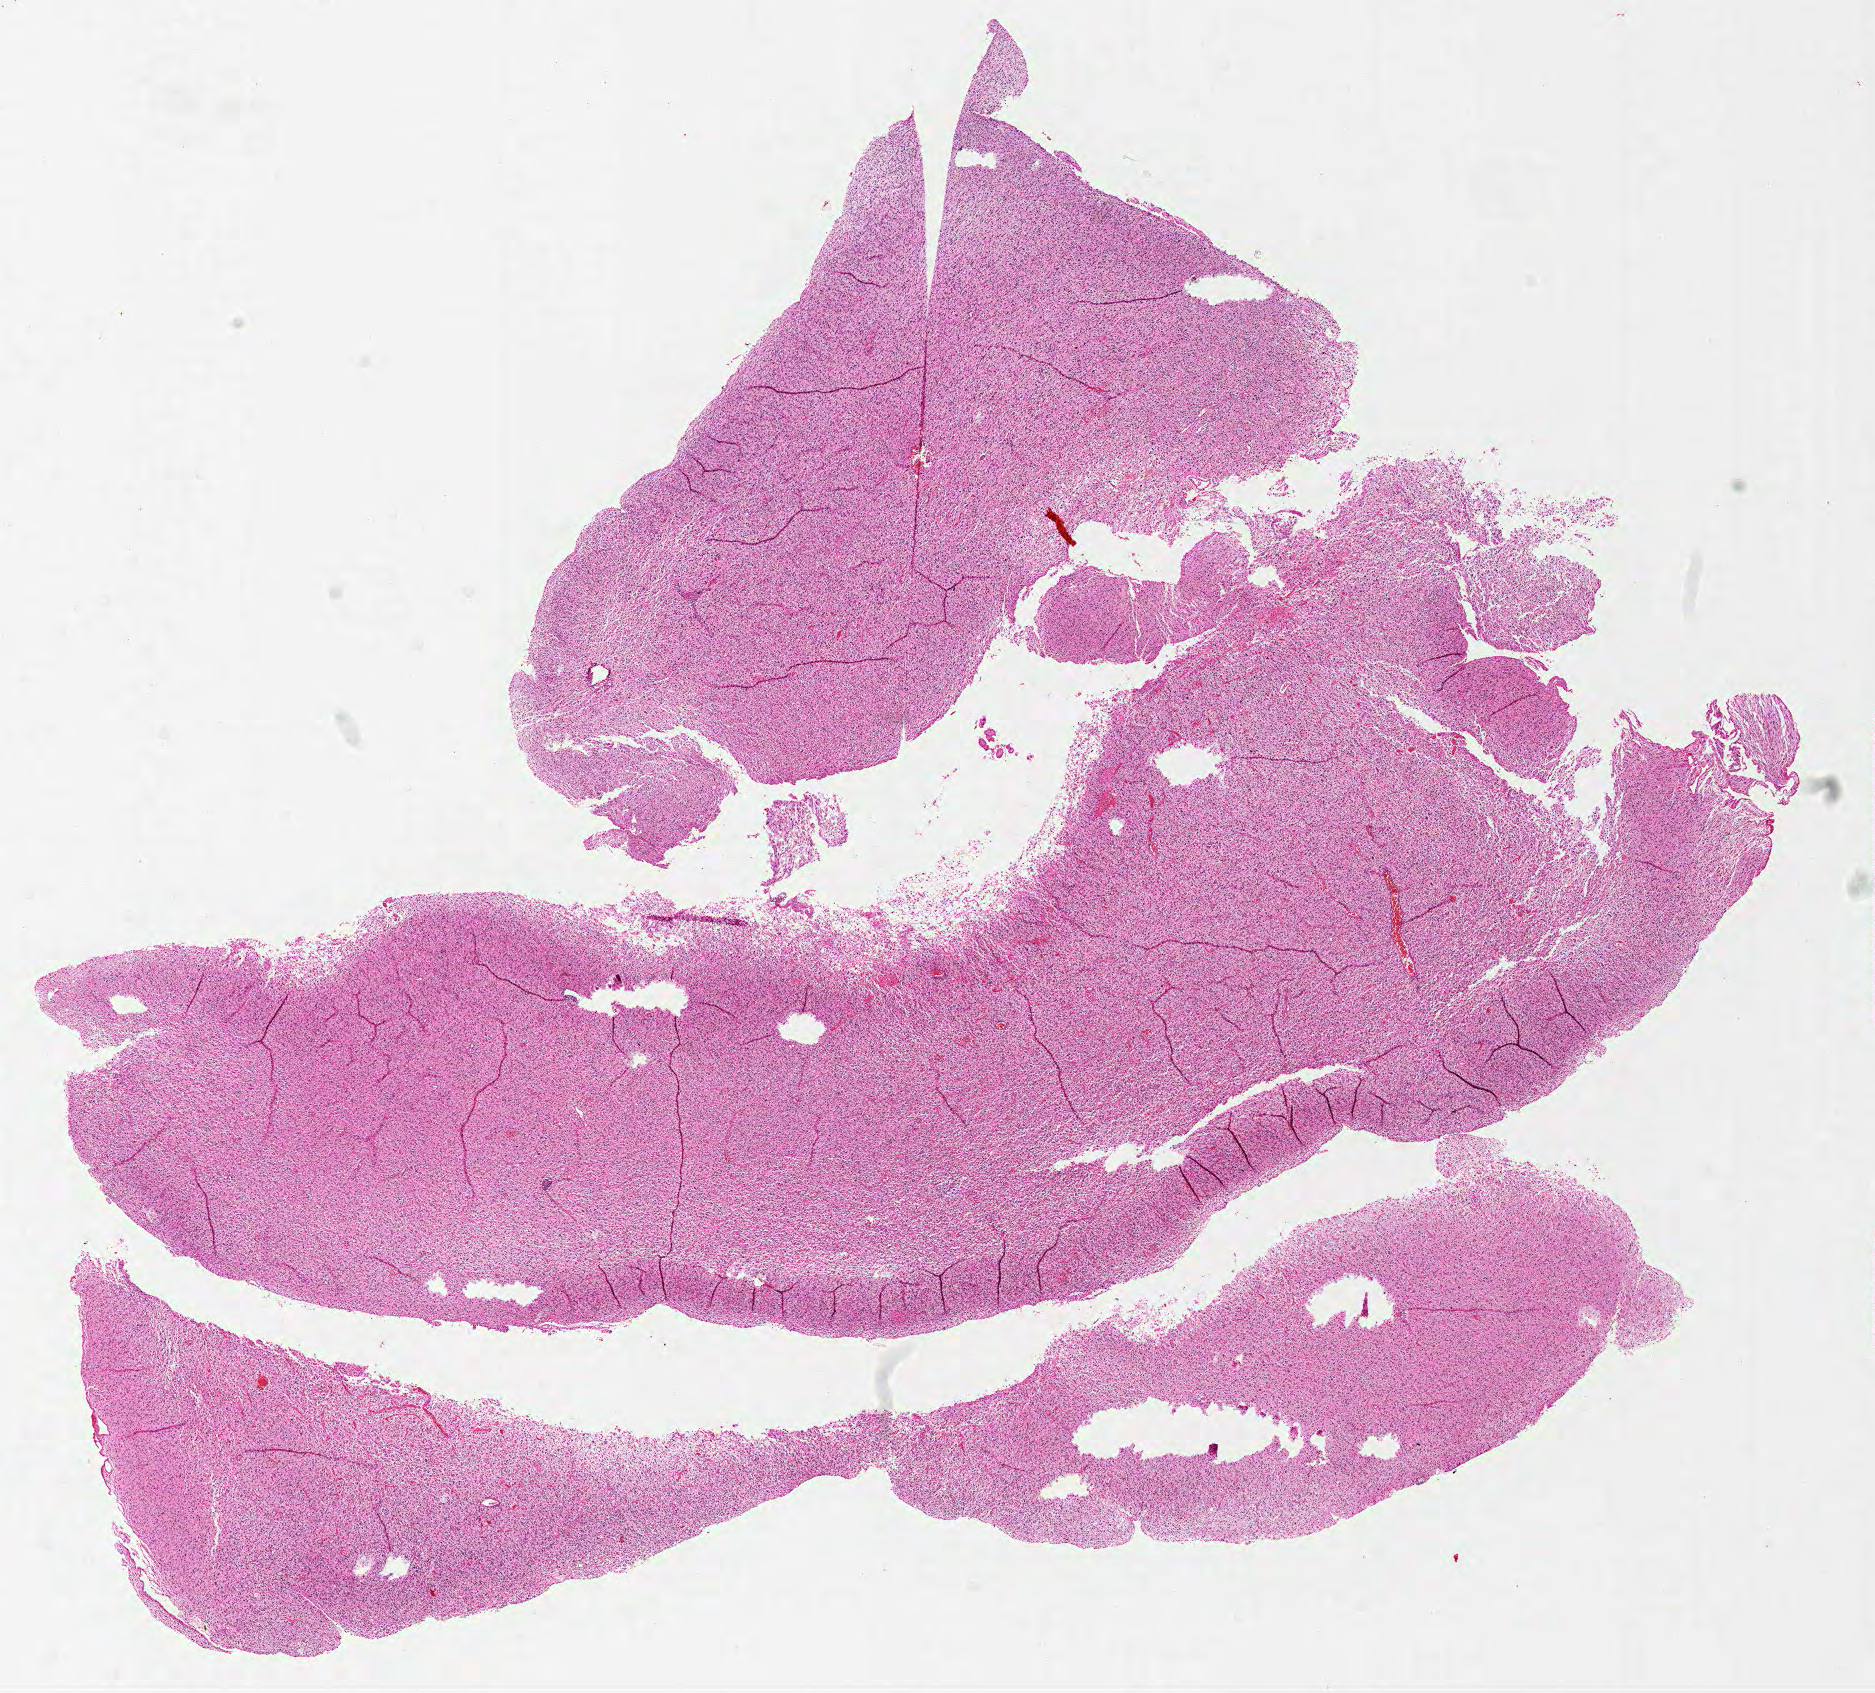
Whole-slide histology image, Hematoxylin and eosin (H&E) stained, a low-resolution overview of the entire scanned area, about 15.0 x 13.5 mm. FFPE section. Brain, primary tumour sample. Female patient; age at initial diagnosis 36 years.
- histologic diagnosis: Glioblastoma